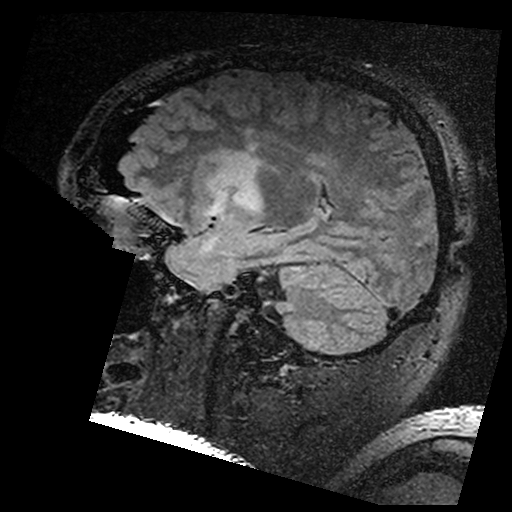
Brain MRI from a brain-tumour surgery series, one sagittal slice. Position 114 of 176 along the scan axis. T2 FLAIR. 1 mm slice thickness. 512 × 512 image matrix, field of view 250 × 250 mm. From the clinical record (not read from this slice): histopathology: Astrocytoma; WHO grade: 3; IDH mutation: yes; tumour location: Left Insular.
Structures marked on this image (expert manual segmentation):
- residual tumour: bounding box <202,146,260,200> (left, top, right, bottom; pixels)